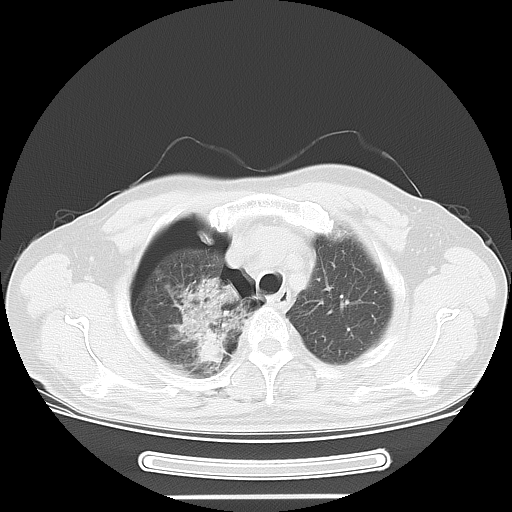
Chest CT, one axial slice. Slice 47 of 57 in the series (ordered by position). Lung window (W 1500 / L -600 HU). 5 mm slice thickness. 512 × 512 image matrix, field of view 376 × 376 mm. Patient: male, 61 years. Case-level facts recorded for this patient, not image findings: clinical TNM (as recorded): T1c N3 M1b.
Structures marked on this image (rectangle marked by the reading radiologist):
- lung tumour (recorded histology: adenocarcinoma): bounding box [x1, y1, x2, y2] px = [162, 278, 245, 372]